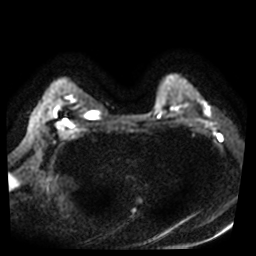
Breast MRI, one axial slice; slice 32 of 40 in the series (ordered by position); diffusion-weighted series; image 2 of 4 stored at this slice position (different b-values; order by instance number); 3 T; 5 mm slice thickness; 256 × 256 image matrix. Female patient.
Outlined on this slice (expert manual segmentation):
- tumour on diffusion-weighted imaging: bounding box [x1, y1, x2, y2] px = [204, 107, 209, 113]